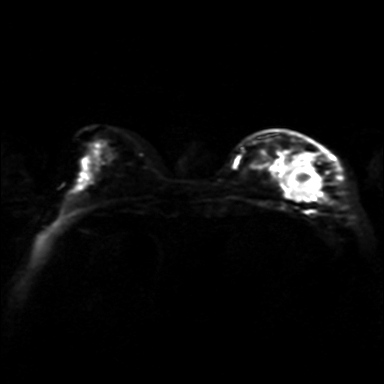
Breast MRI, one axial slice. Position 12 of 36 along the scan axis. Diffusion-weighted series; image 2 of 4 stored at this slice position (different b-values; order by instance number). 3 T. 4 mm slice thickness. 384 × 384 image matrix, field of view 320 × 320 mm. Female patient.
Annotated regions visible in this slice (expert manual segmentation):
- tumour on diffusion-weighted imaging: box from (x=284, y=168) to (x=317, y=201) px